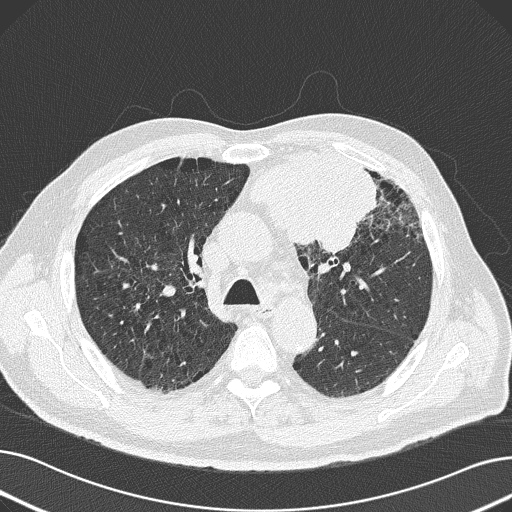
Axial slice from a low-dose chest CT screening exam, baseline annual screen, lung window (W 1500 / L -600 HU), 2 mm slice thickness, lung (sharp) reconstruction kernel (B50f), 120 kVp, slice 63 of 165 in the series, 512 × 512 image matrix, field of view 370 × 370 mm. Male participant, aged 69 years at enrolment. Former smoker at enrolment.
Expert-annotated lung lesion, bounding box (x1, y1, x2, y2) in pixels: (230, 142, 381, 252). The exam's reader record, not a measurement of the box and not confirmed to be the same lesion: non-calcified nodule or mass ≥4 mm, left upper lobe, 6 × 10 mm, spiculated (stellate) margins, soft tissue attenuation. Official screen result: positive, change unspecified: nodule(s) >= 4 mm or enlarging nodule(s), mass(es), or other non-specific abnormalities suspicious for lung cancer. Participant outcome: lung cancer diagnosed 20 days after this screen — non-small cell carcinoma, left upper lobe, poorly differentiated (G3), stage IB (AJCC 6th edition), 100 mm at pathology.